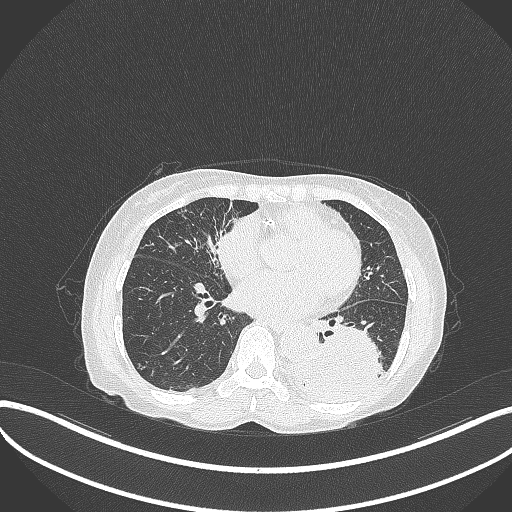
Chest CT, one axial slice; position 127 of 370 along the scan axis; reconstruction kernel B70f; lung window (W 1500 / L -600 HU); 1 mm slice thickness; 512 × 512 image matrix. Patient: female, 78 years. Case-level facts recorded for this patient, not image findings: clinical TNM (as recorded): T3 N0 M1.
Outlined on this slice (bounding box drawn by a radiologist):
- lung tumour (recorded histology: squamous cell carcinoma): bounding box <287,318,388,403> (left, top, right, bottom; pixels)